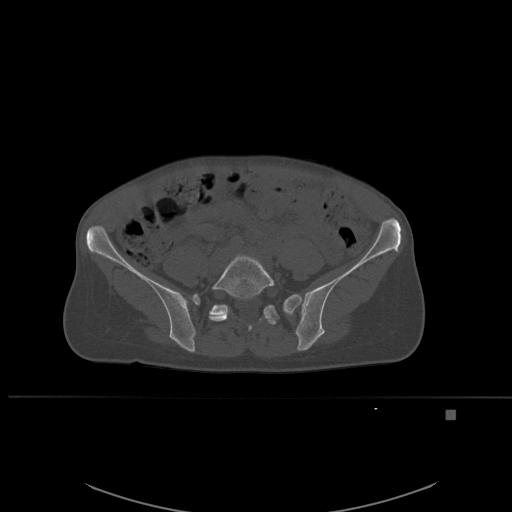
CT including the spine, one axial slice. Position 168 of 537 along the scan axis. Bone window (W 1800 / L 400 HU). 1.5 mm slice thickness. 512 × 512 image matrix. Female patient, age 45 years. Case-level facts recorded for this patient, not image findings: primary cancer: lung.
Structures marked on this image (semi-automatically segmented with operator editing):
- L5 vertebra: bounding box <209,254,276,331> (left, top, right, bottom; pixels)